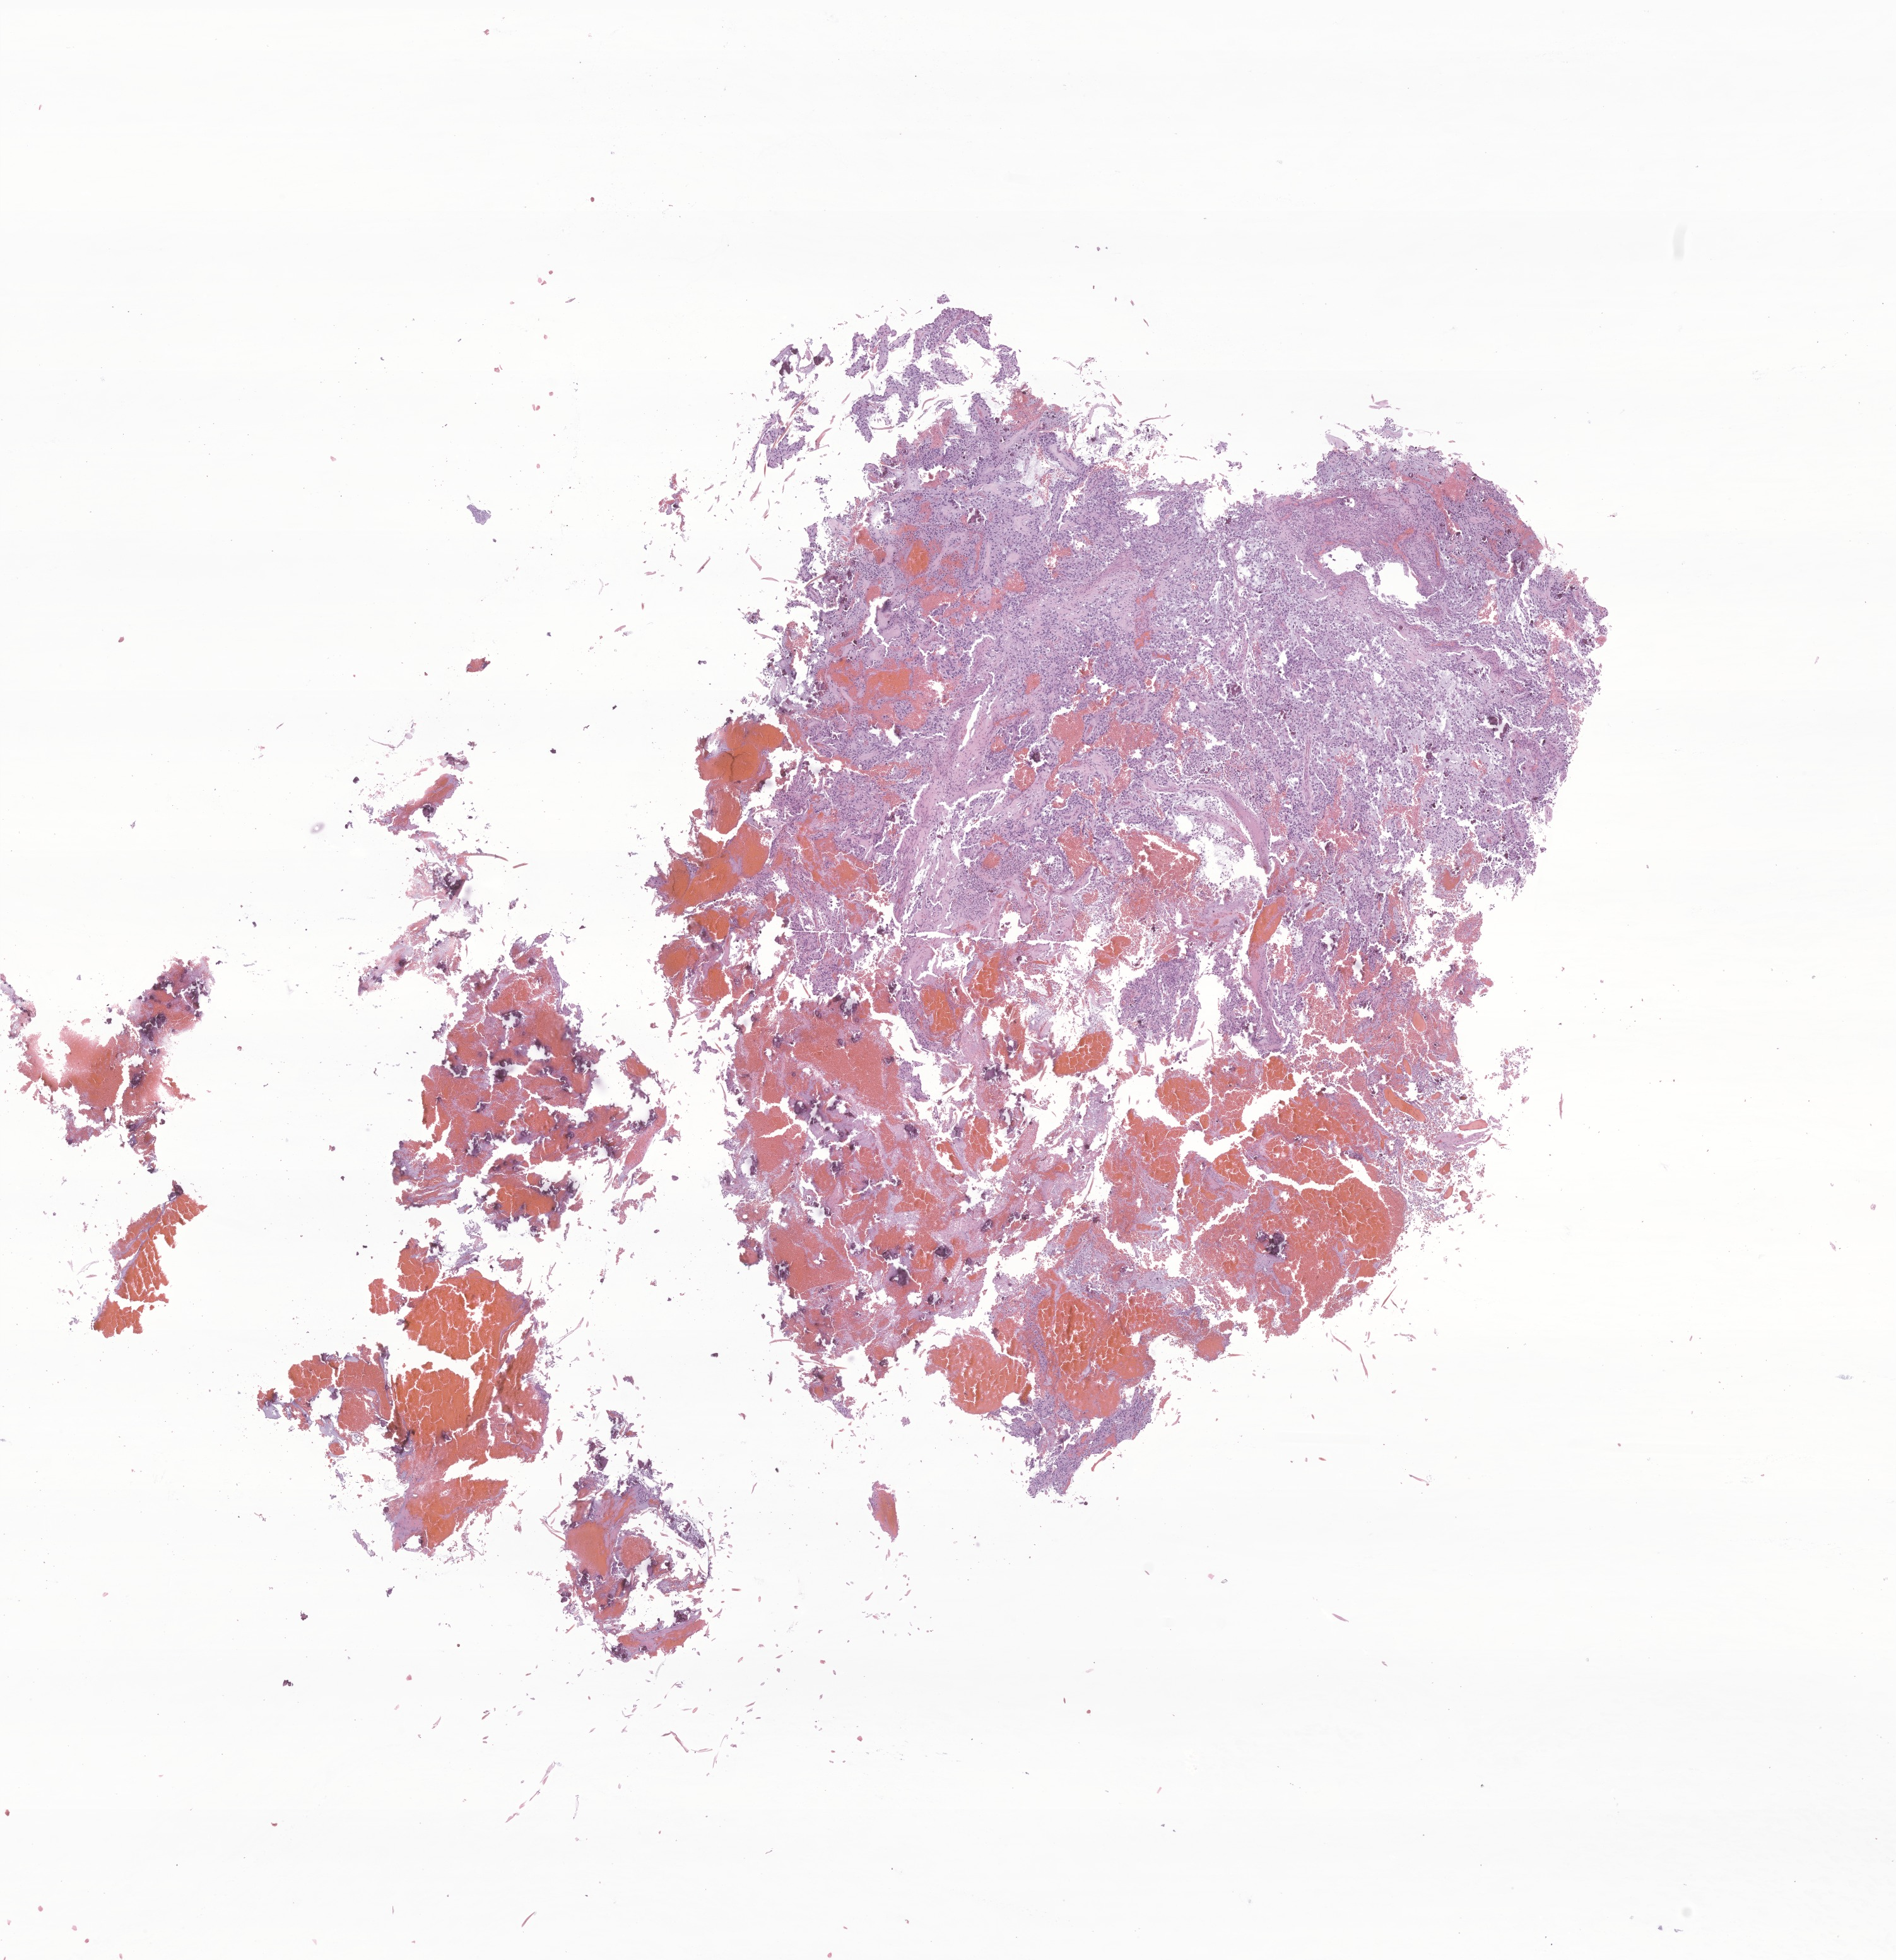
Digitized hematoxylin and eosin (H&E)-stained section of tumor tissue from the temporal lobe — shown as a low-resolution overview of the whole scanned area (about 12.7 x 13.1 mm), formalin-fixed paraffin-embedded section. Male patient, age 205 months (17 years 1 month).
Diagnosis: Glioma, malignant.